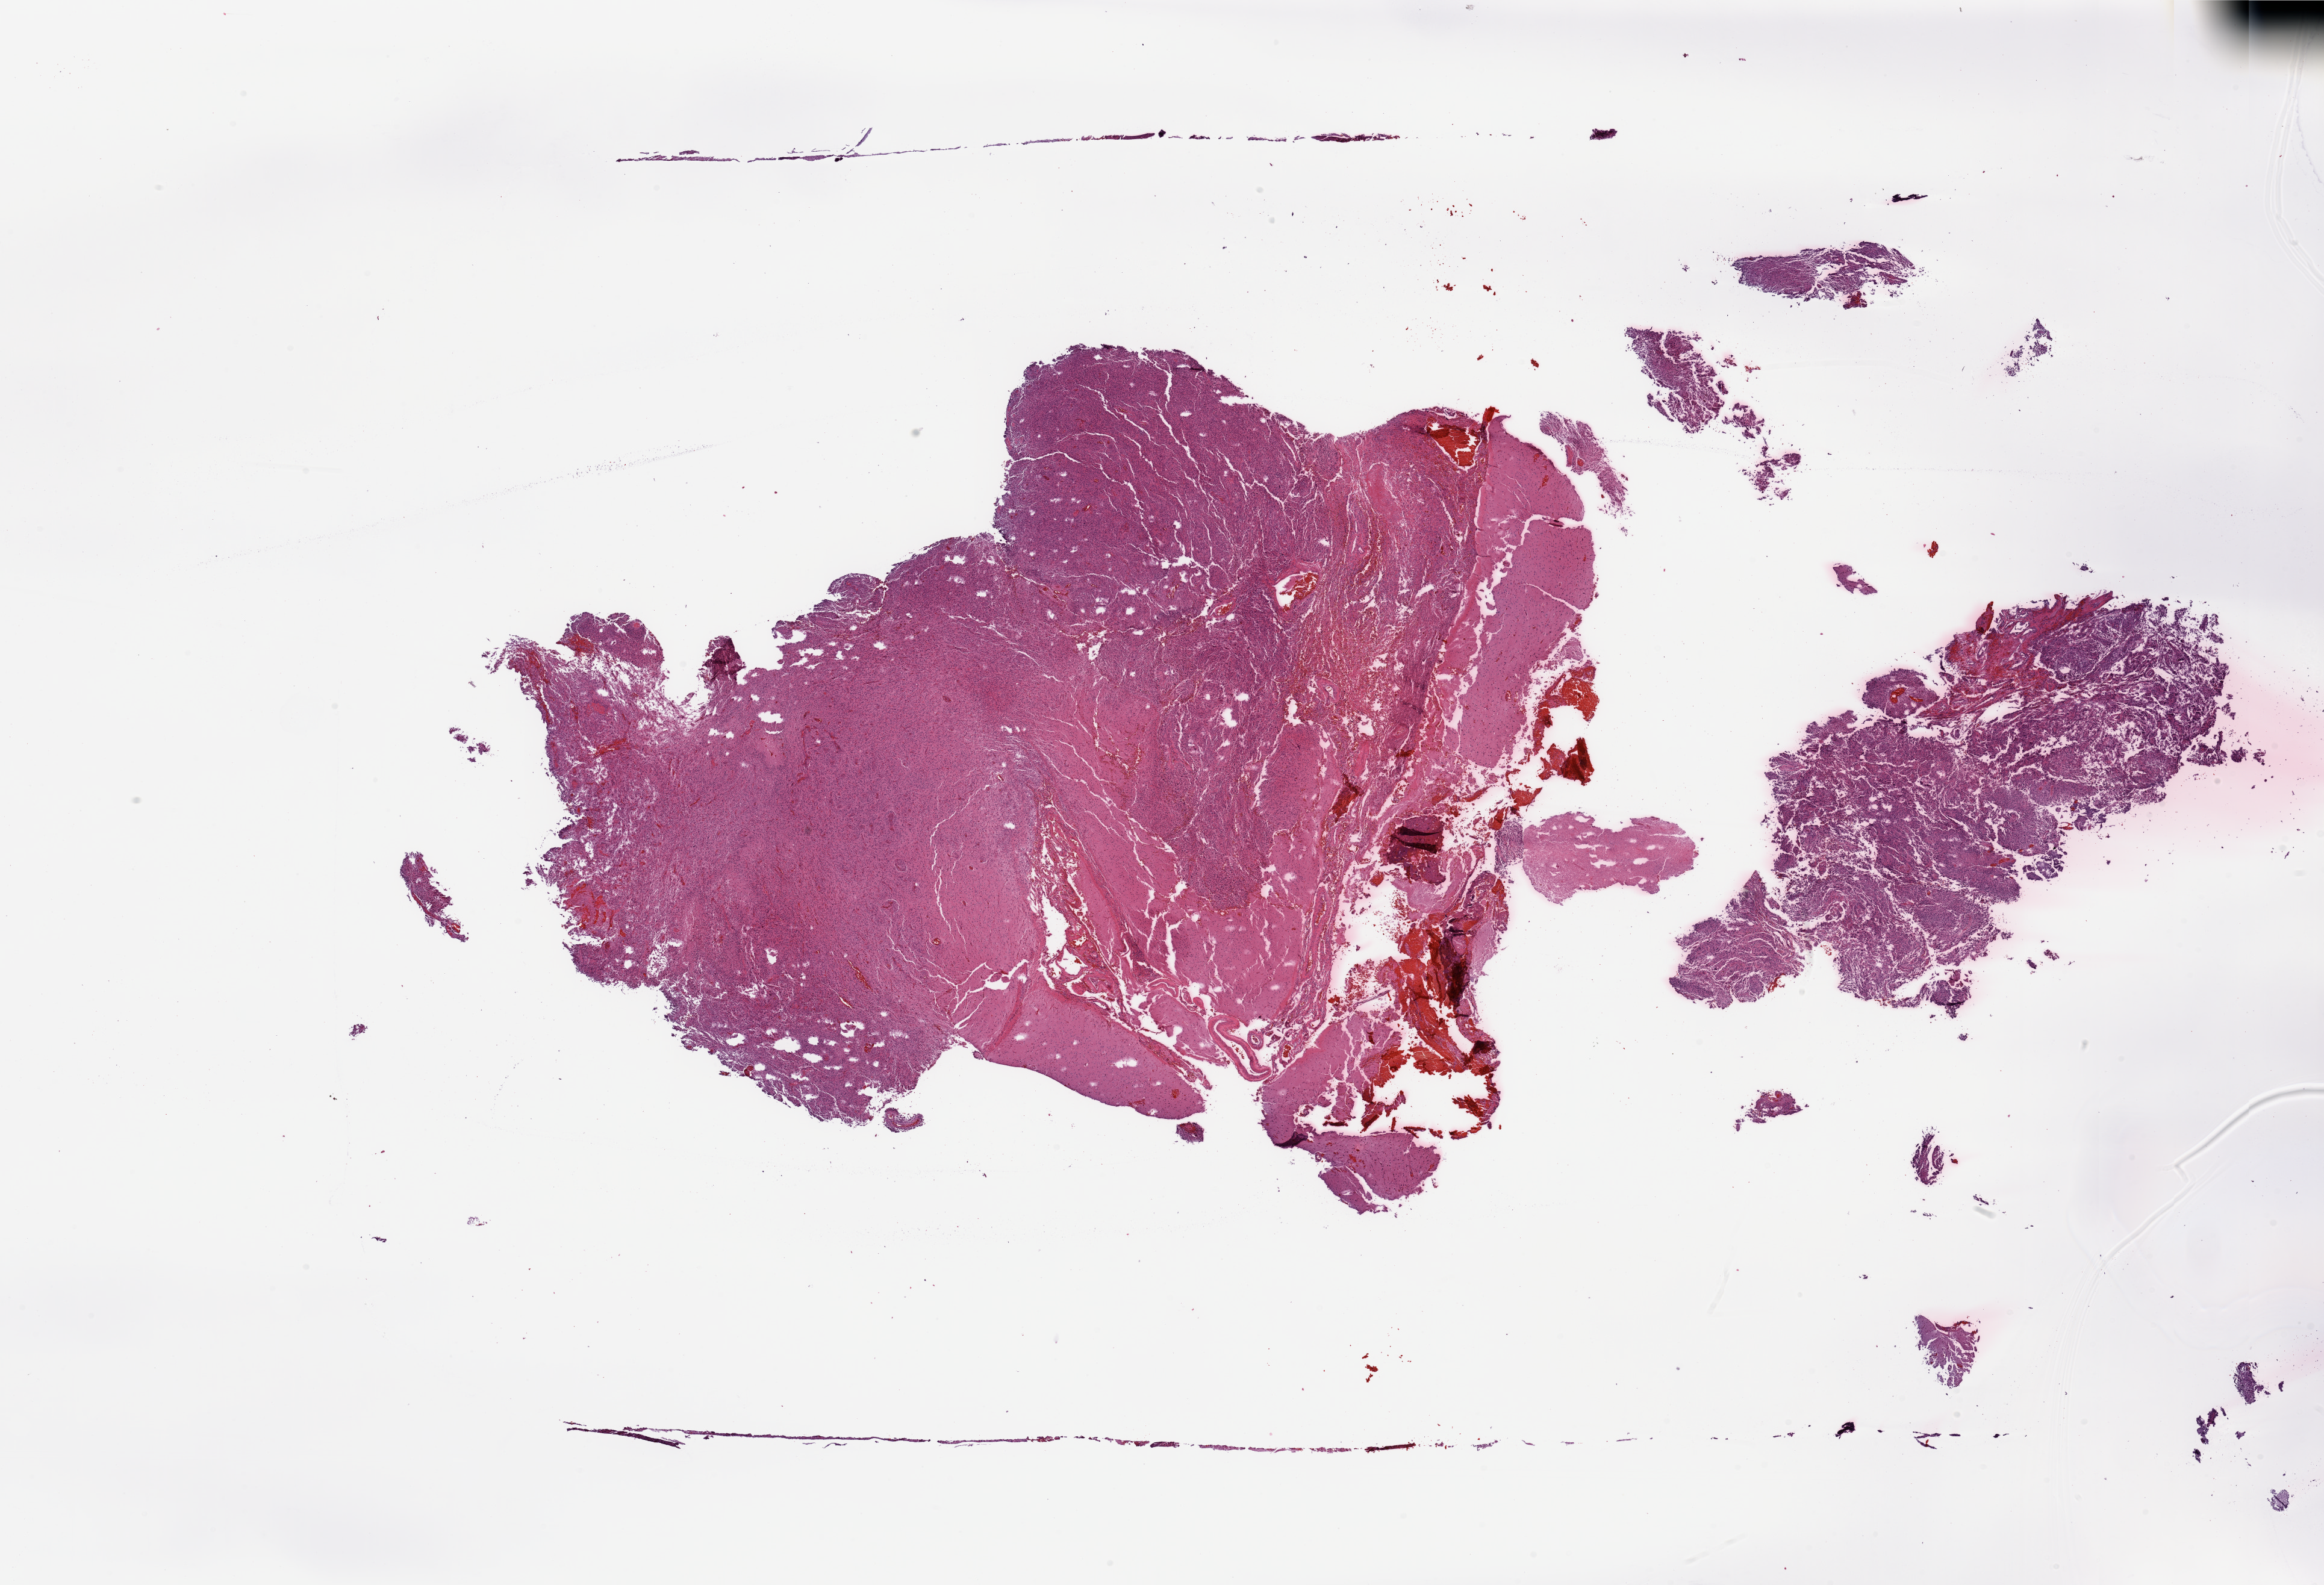
H&E-stained whole-slide image — shown as a low-resolution overview of the whole scanned area (about 30.5 x 20.8 mm); tumour tissue sample, sampled site: brain. 75-year-old male patient. Composition of this section per pathologist review: tumour nuclei 80%, necrosis 20%.
Histologic diagnosis: Glioblastoma. Primary tumour site (as recorded): temporal lobe.